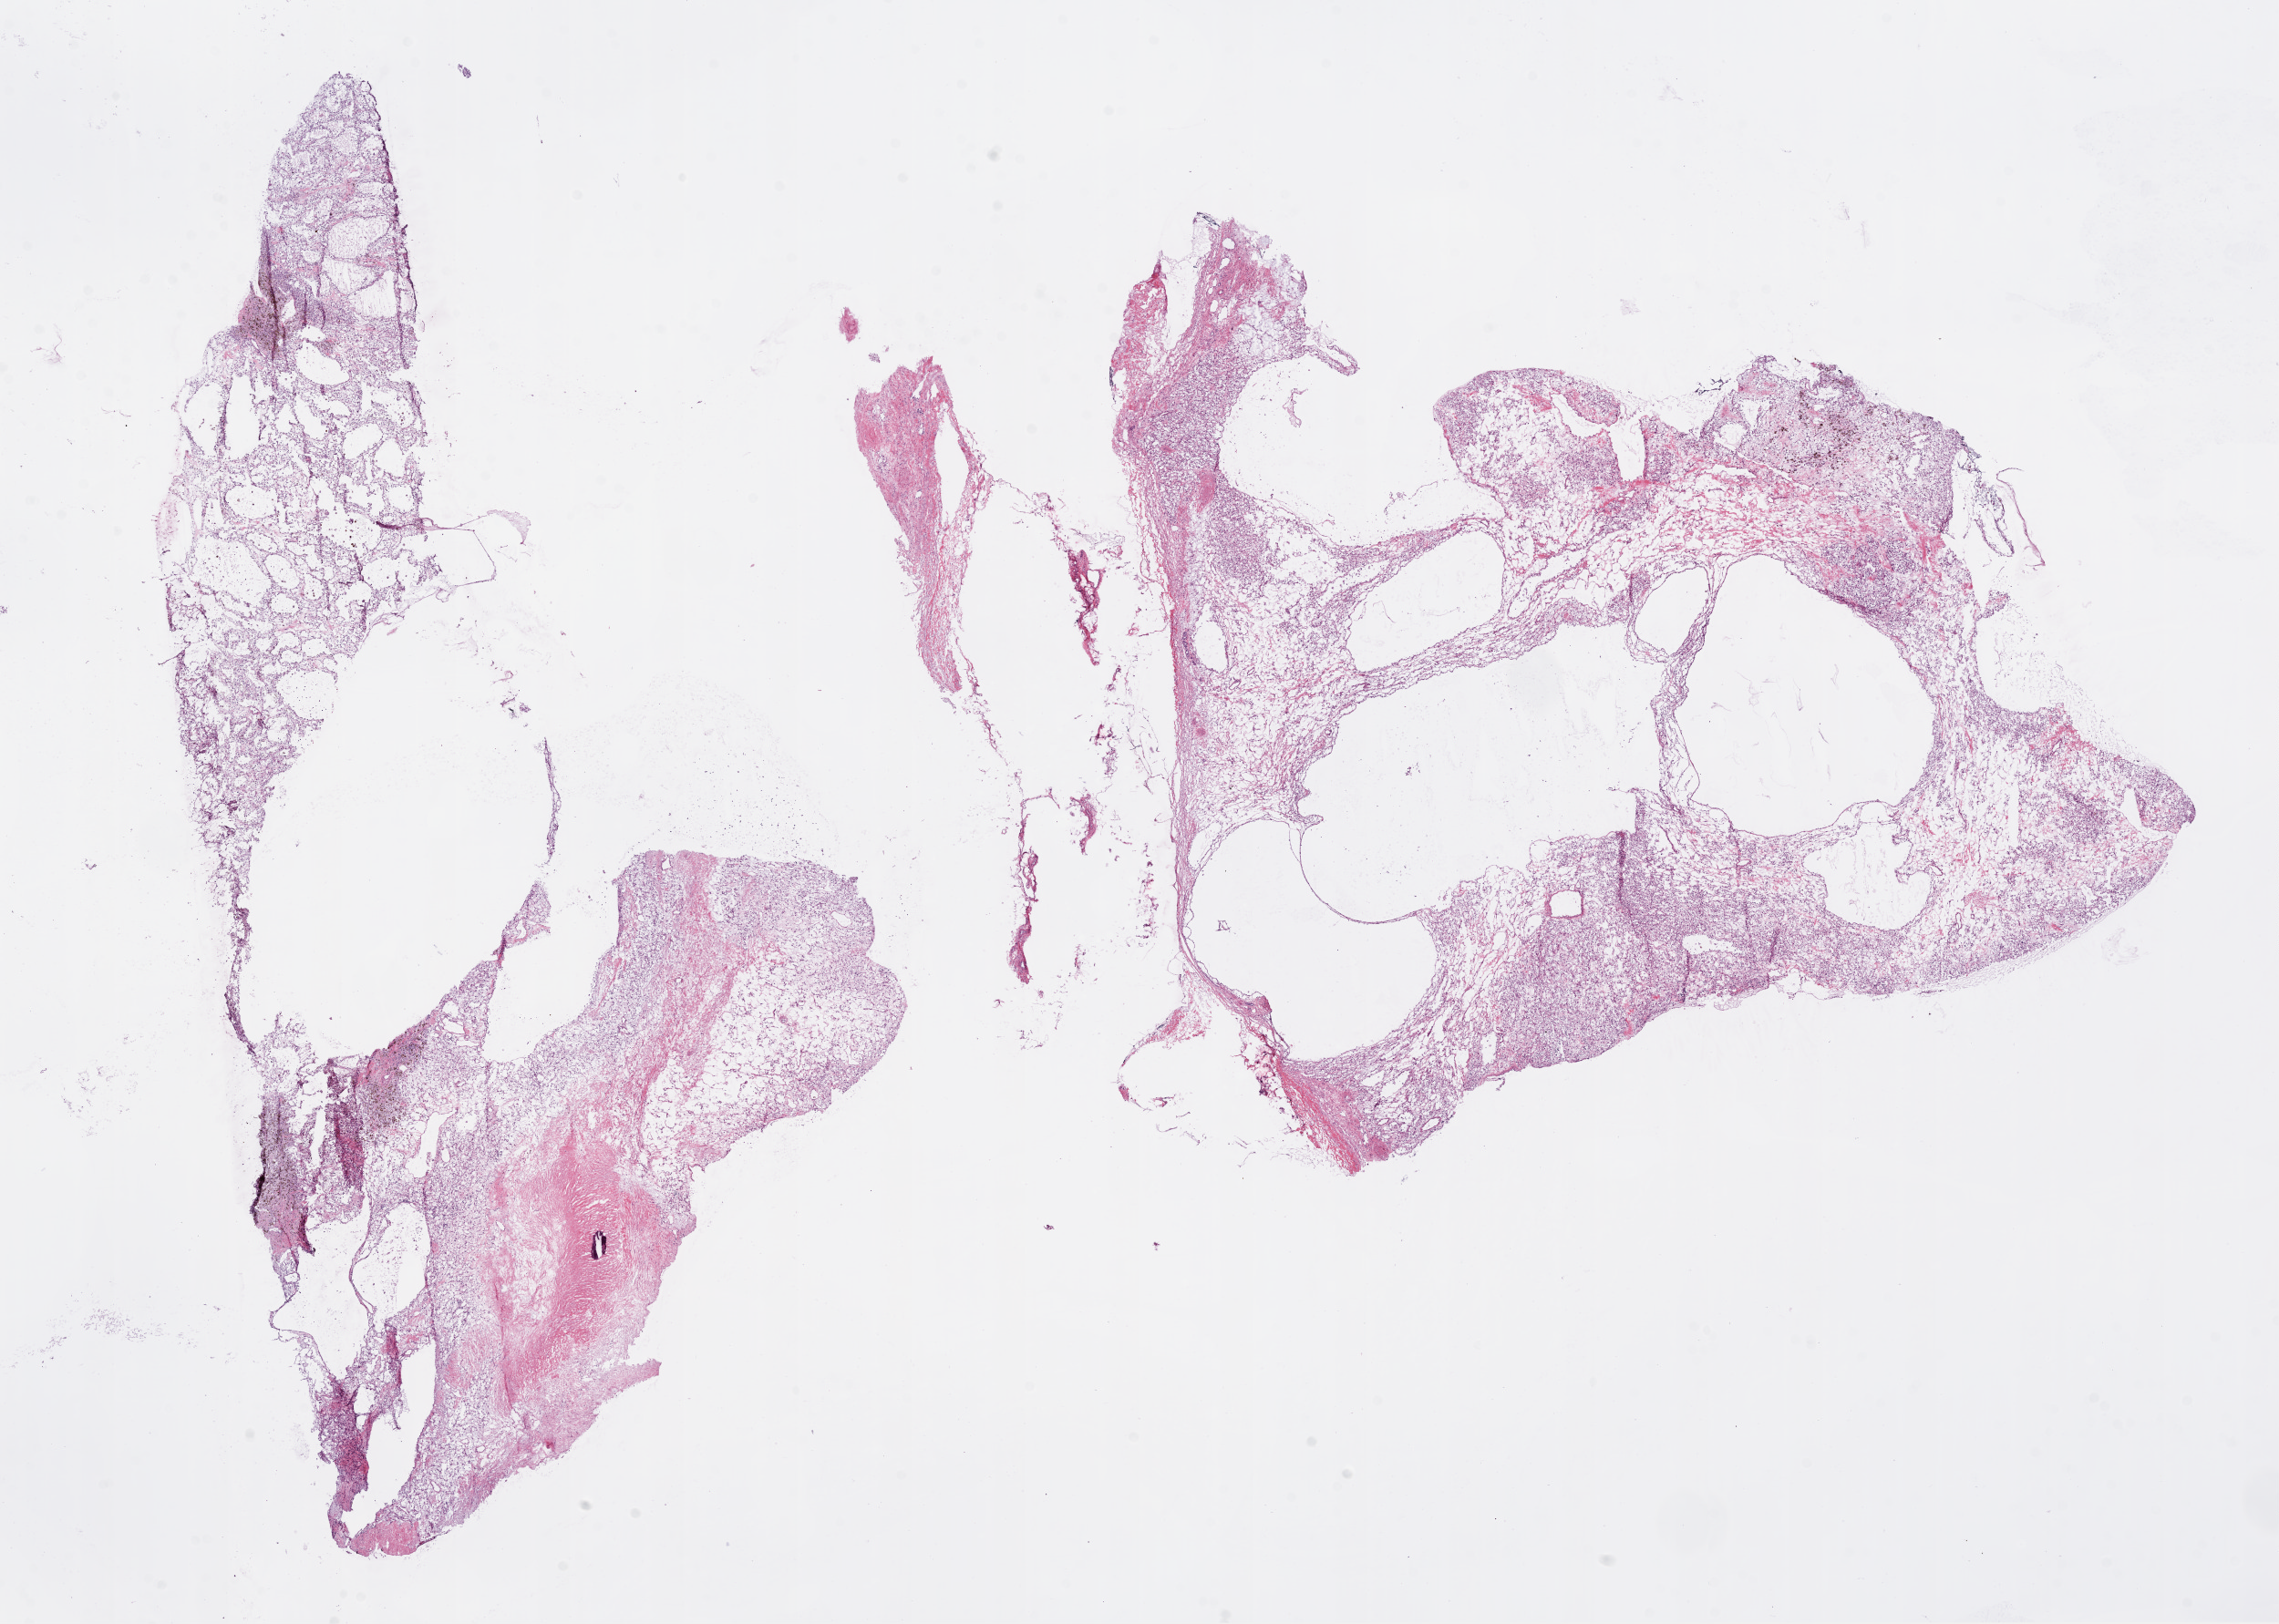
Digitized Hematoxylin and eosin (H&E) stained tissue section (whole slide) — low-resolution overview of the scanned area, about 20.1 x 14.3 mm. Frozen section from the bottom of the tissue portion. Sample: primary tumour, kidney. Male patient; age at initial diagnosis 57 years. Histologic grade: G2 (moderately differentiated). Slide review estimates, as recorded: tumour cells 90%, tumour nuclei 90%, normal cells 0%, stromal cells 10%, necrosis 0%.
AJCC pathologic stage: I. TNM: T1a NX M0. Laterality: left. Pathologic diagnosis: Clear cell adenocarcinoma, NOS.